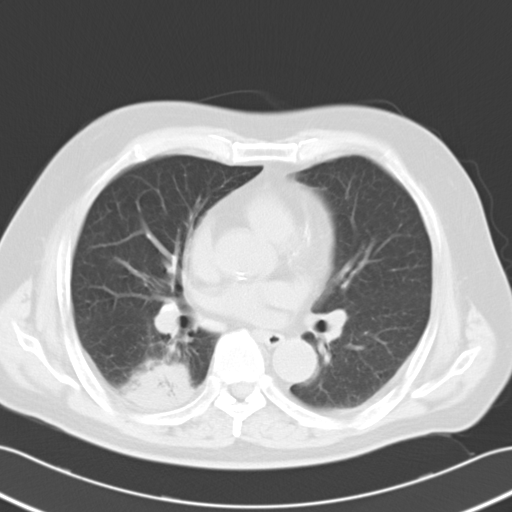
Chest CT, one axial slice. Position 11 of 25 along the scan axis. Lung window (W 1500 / L -600 HU). 10 mm slice thickness. 512 × 512 image matrix, field of view 353 × 353 mm. Male patient, age 70 years. From the clinical record (not read from this slice): clinical TNM (as recorded): T2 N0 M0; histopathological grade: G2.
Outlined on this slice (bounding box drawn by a radiologist):
- lung tumour (recorded histology: adenocarcinoma): box from (x=127, y=359) to (x=201, y=419) px